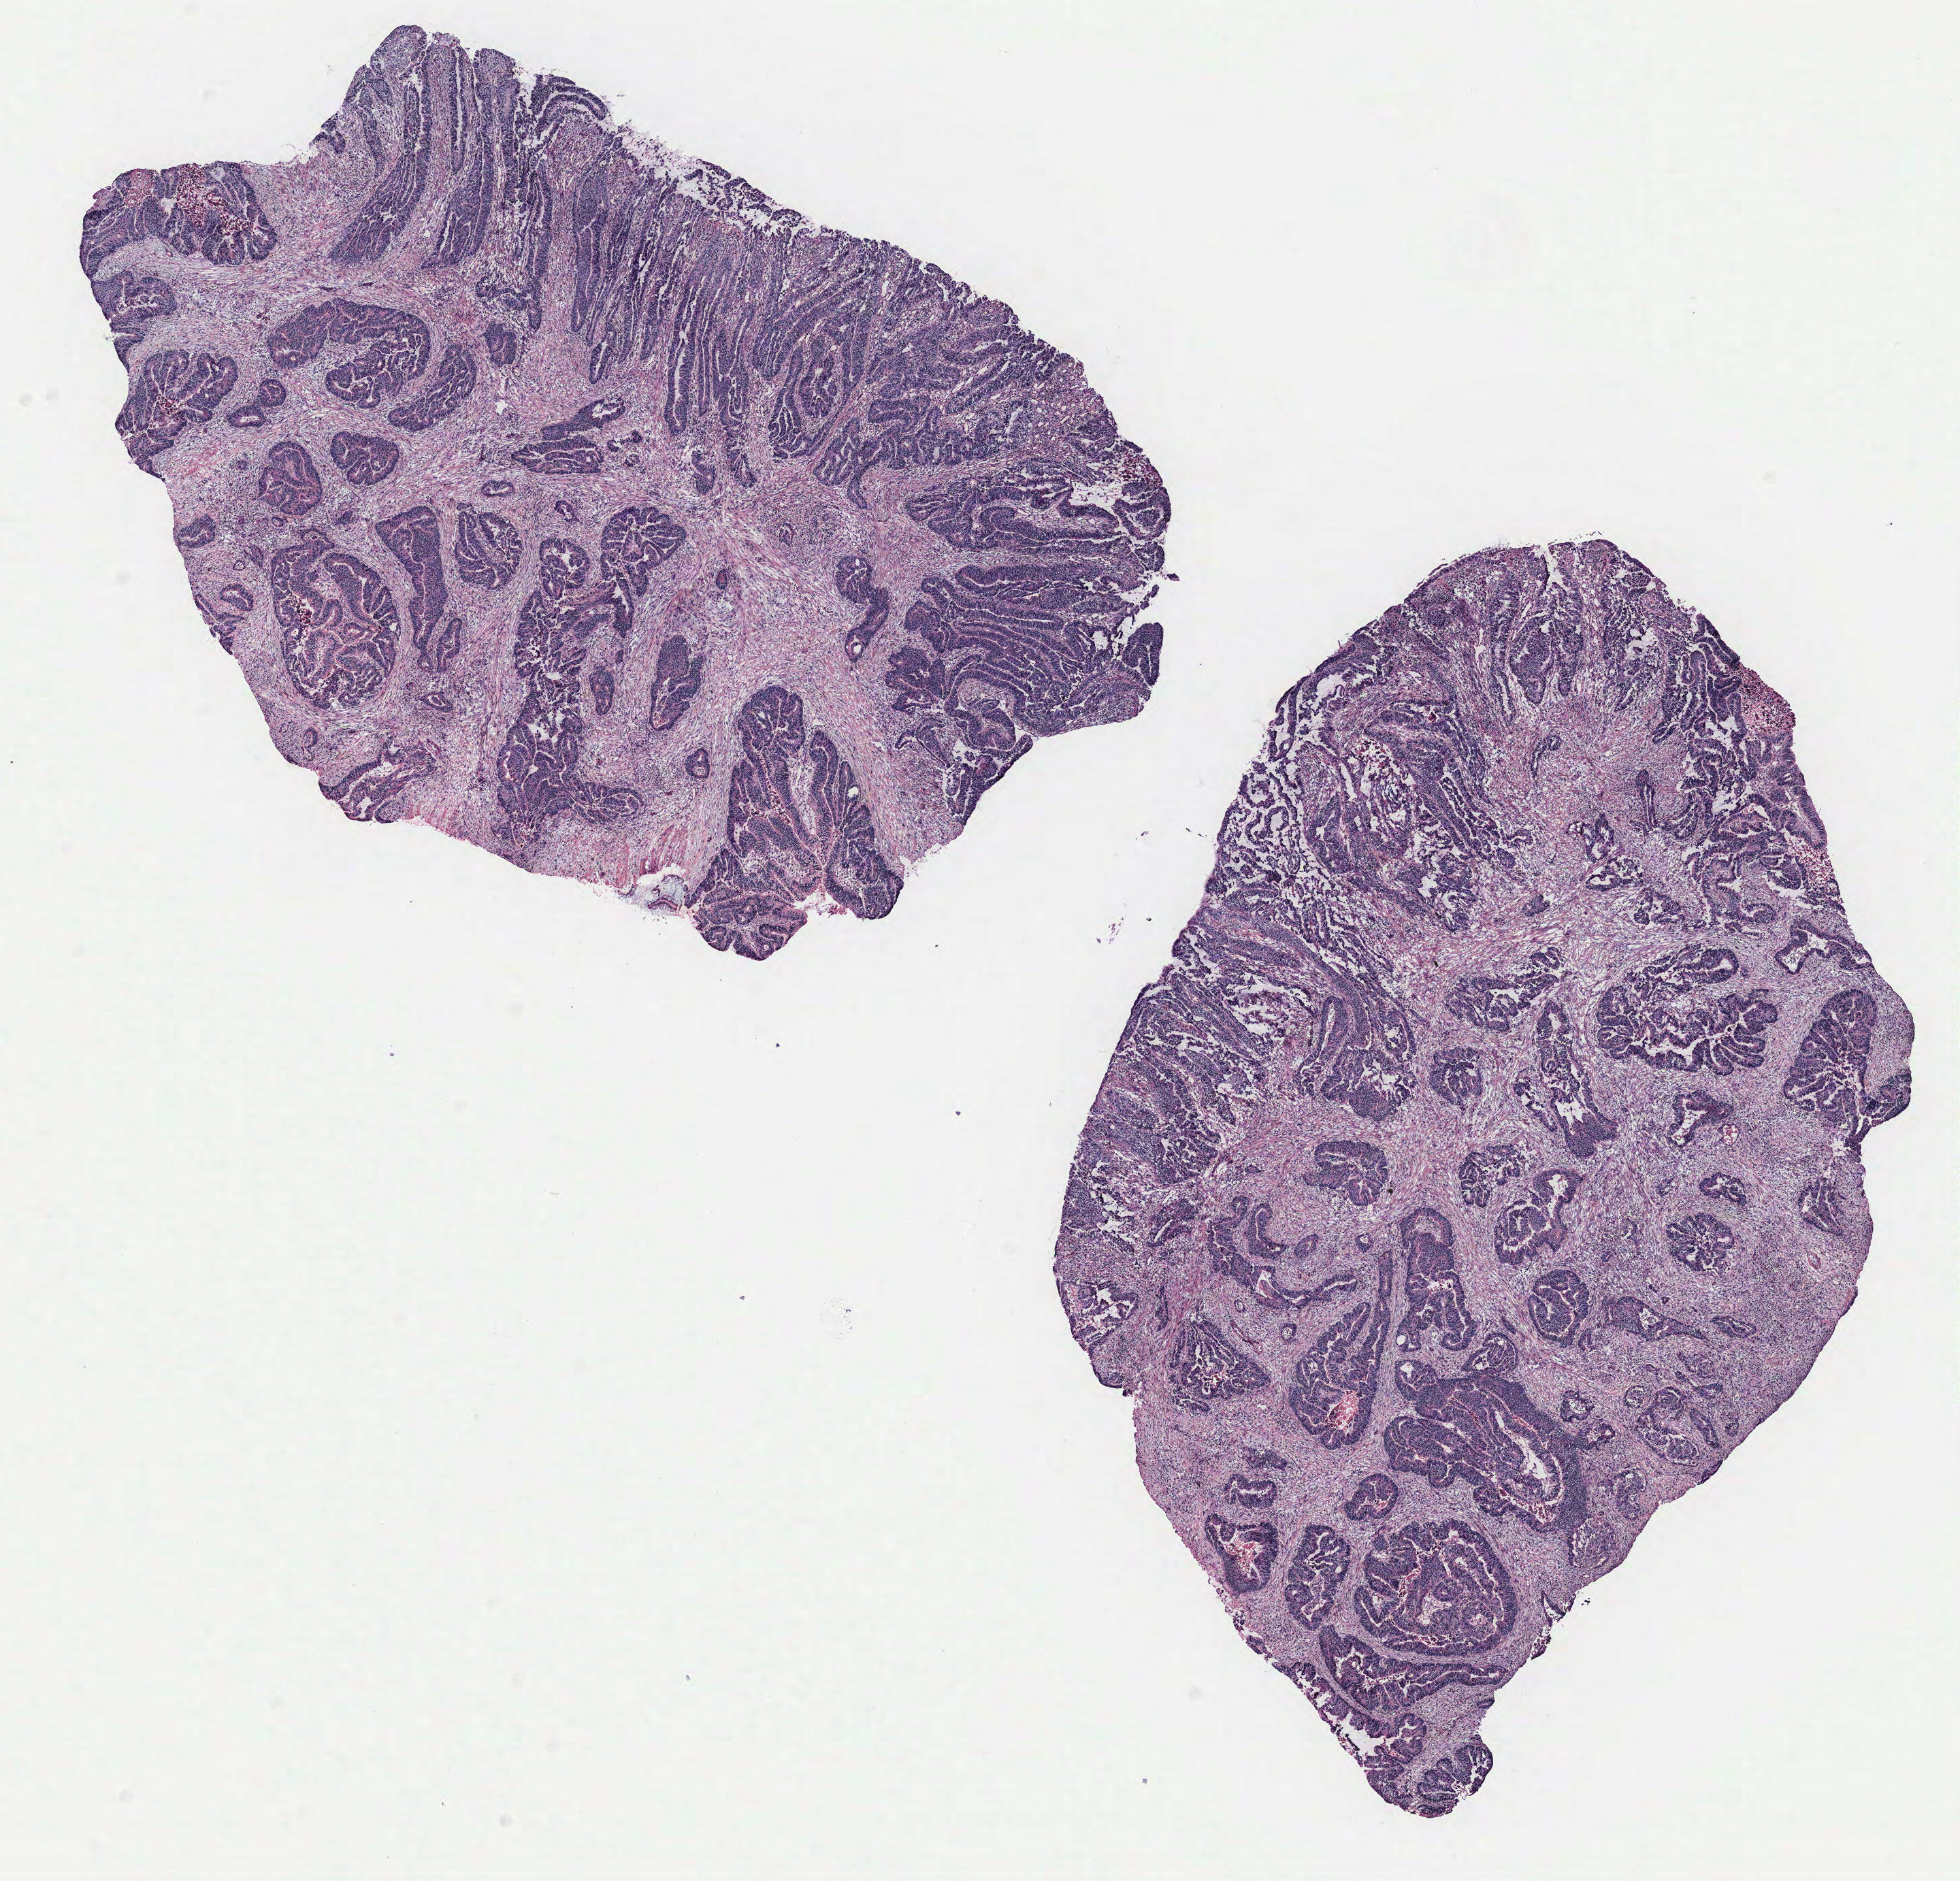
Whole-slide histology image, H&E, shown as a low-resolution overview of the whole scanned area (about 11.5 x 11.1 mm), colon, tissue type not recorded. Male patient.
Patient diagnosis: Adenocarcinoma, NOS.